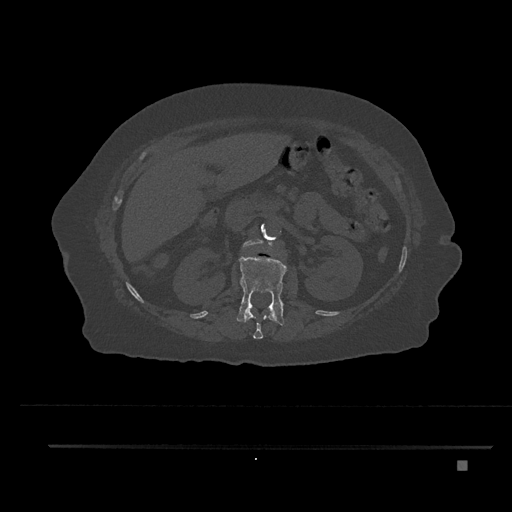
CT including the spine, one axial slice. Slice 227 of 797 in the series (ordered by position). Reconstruction kernel Br40s/3. 120 kVp. Bone window (W 1800 / L 400 HU). 0.5 mm slice thickness. 512 × 512 image matrix, field of view 437 × 437 mm. Patient: female, 76 years. From the clinical record (not read from this slice): primary cancer: lung; vertebrae with lytic lesions (as recorded): T11, L3.
Structures marked on this image (semi-automatically segmented with operator editing):
- L1 vertebra: box from (x=237, y=255) to (x=287, y=326) px
- L2 vertebra: (x=243, y=239)–(x=273, y=253)
- T12 vertebra: (x=244, y=307)–(x=277, y=339)